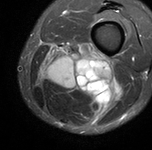
MRI of an extremity soft-tissue mass, one axial slice; STIR; MR volume resampled by the dataset authors to the PET/CT grid (not the native acquisition matrix); 3.27 mm slice thickness; 152 × 150 image matrix, field of view 148 × 146 mm. Male patient. From the clinical record (not read from this slice): histological type: undifferentiated pleomorphic liposarcoma; grade: high; site of the primary tumour: left thigh.
Outlined on this slice (expert contour drawn on MRI and transferred to this co-registered scan by the dataset authors):
- gross tumour volume including surrounding oedema: bounding box <39,41,120,118> (left, top, right, bottom; pixels)